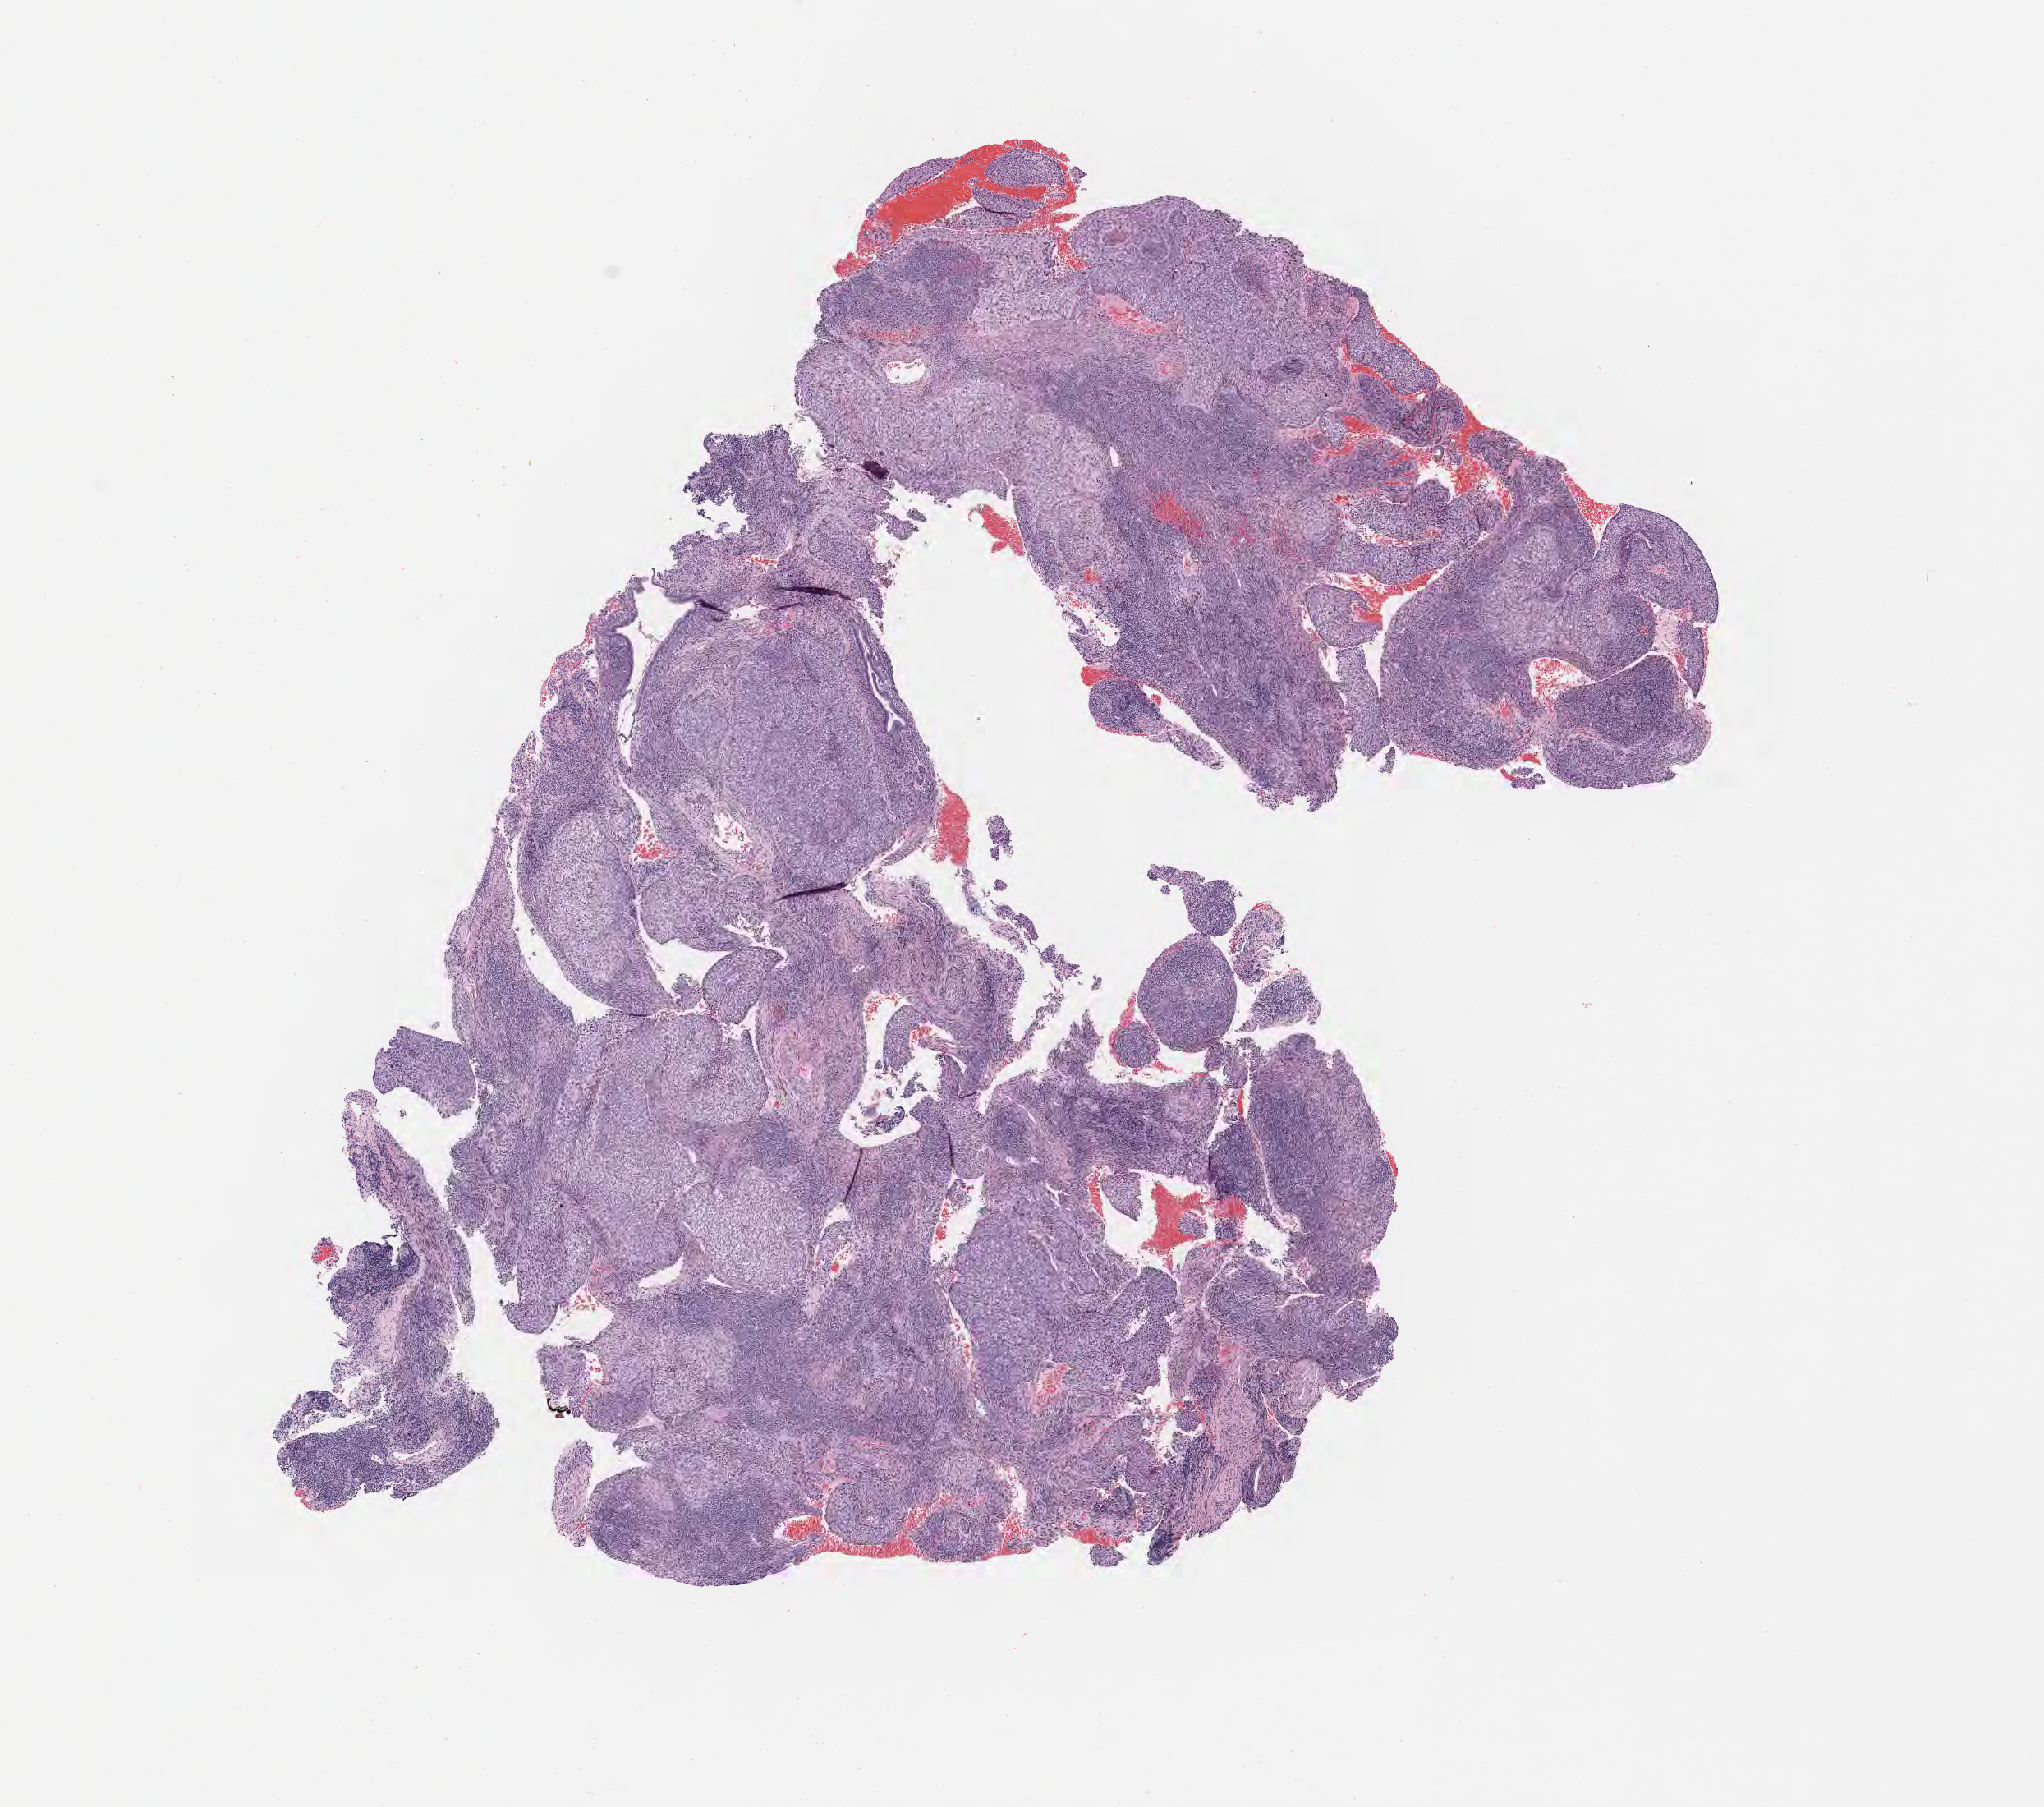
Digitized haematoxylin and eosin-stained section, whole scanned area (about 10.1 x 8.9 mm) shown as a low-resolution overview. Tumor tissue. Anatomic site: cervix. Patient: female, 50 years old.
Diagnosis: Squamous cell carcinoma, large cell, nonkeratinizing, NOS.